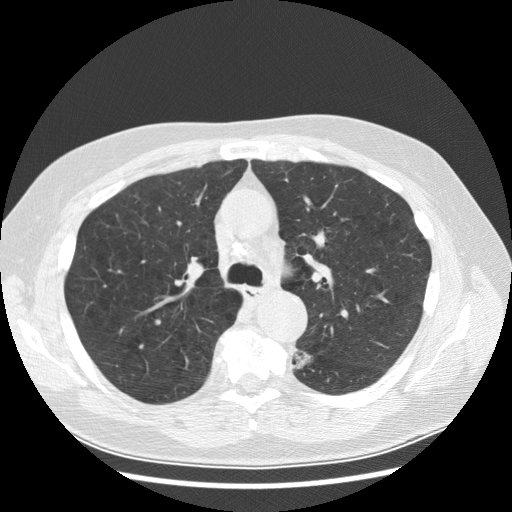
Low-dose screening chest CT, one axial slice; reconstruction kernel STANDARD; 120 kVp; lung window (W 1500 / L -600 HU); 512 × 512 image matrix, field of view 370 × 370 mm.
Structures marked on this image (outlined manually by an expert reader):
- lesion 1 (tumor, lower lobe of left lung): box from (x=295, y=352) to (x=311, y=369) px